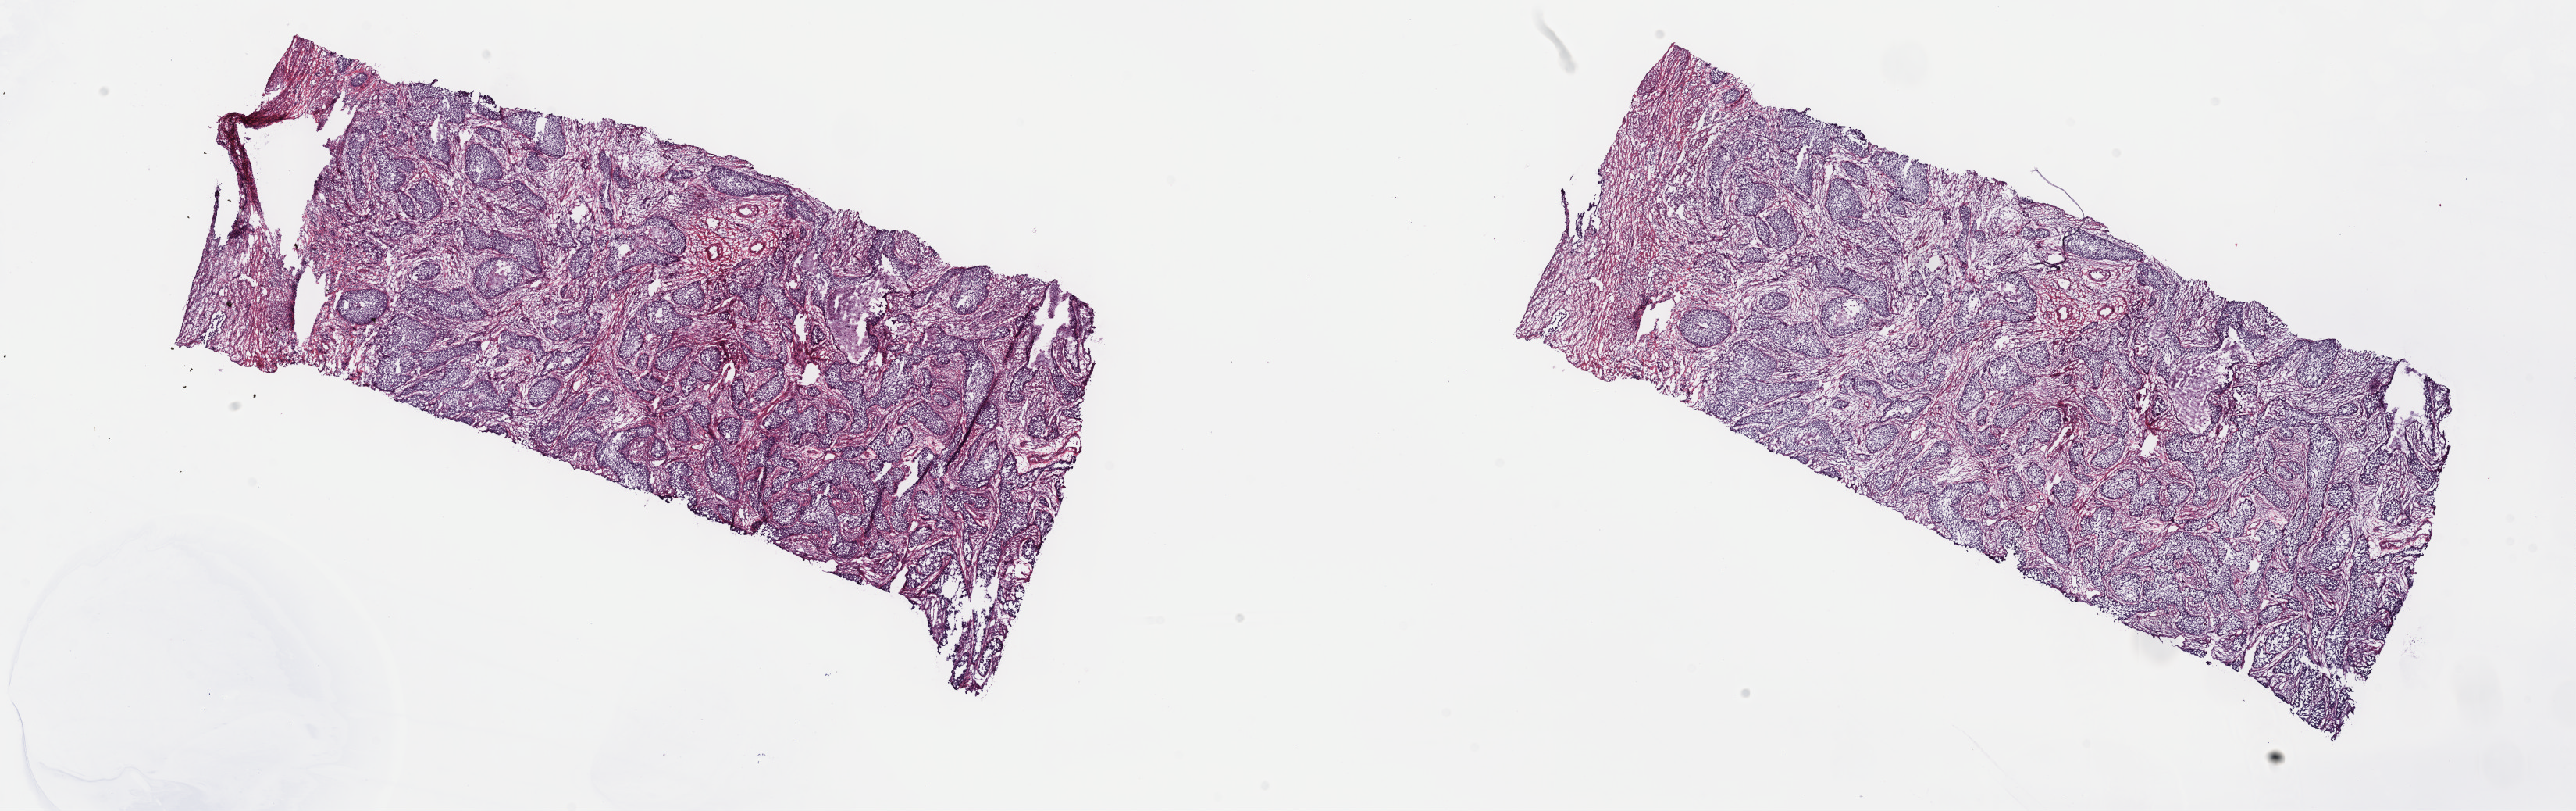
Digitized Hematoxylin and eosin (H&E) stained tissue section (whole slide) — a low-resolution overview of the entire scanned area, about 26.7 x 8.4 mm (slide scanned at 40x). Frozen section from the top of the tissue portion. Cervix, primary tumour sample. Female patient; age at initial diagnosis 49 years. Histologic grade: G3 (poorly differentiated). Pathologist review of this section (percent, as recorded): tumour cells 70%, tumour nuclei 70%, normal cells 8%, stromal cells 20%, necrosis 2%. Infiltration values recorded for this section: lymphocyte infiltration 5%, monocyte infiltration 2%, neutrophil infiltration 2%.
* FIGO stage: IIB
* histologic diagnosis: Adenosquamous carcinoma